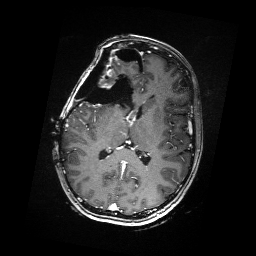
Brain MRI from a brain-tumour surgery series, one axial slice; slice 85 of 176 in the series (ordered by position); T1-weighted post-contrast; 256 × 256 image matrix, field of view 256 × 256 mm. Case-level facts recorded for this patient, not image findings: histopathology: Metastatic Carcinoma from Breast primary; tumour location: Right Frontal.
Annotated regions visible in this slice (expert manual segmentation):
- residual tumour: bounding box <88,68,117,103> (left, top, right, bottom; pixels)